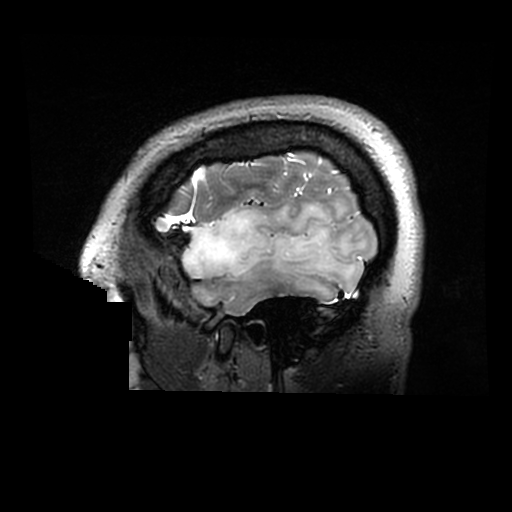
Brain MRI from a brain-tumour surgery series, one sagittal slice. Position 244 of 320 along the scan axis. 0.6 mm slice thickness. 512 × 512 image matrix, field of view 240 × 240 mm. From the clinical record (not read from this slice): histopathology: Astrocytoma; WHO grade: 2; IDH mutation: yes.
Outlined on this slice (manually delineated by an expert):
- tumour: bounding box <182,201,355,297> (left, top, right, bottom; pixels)